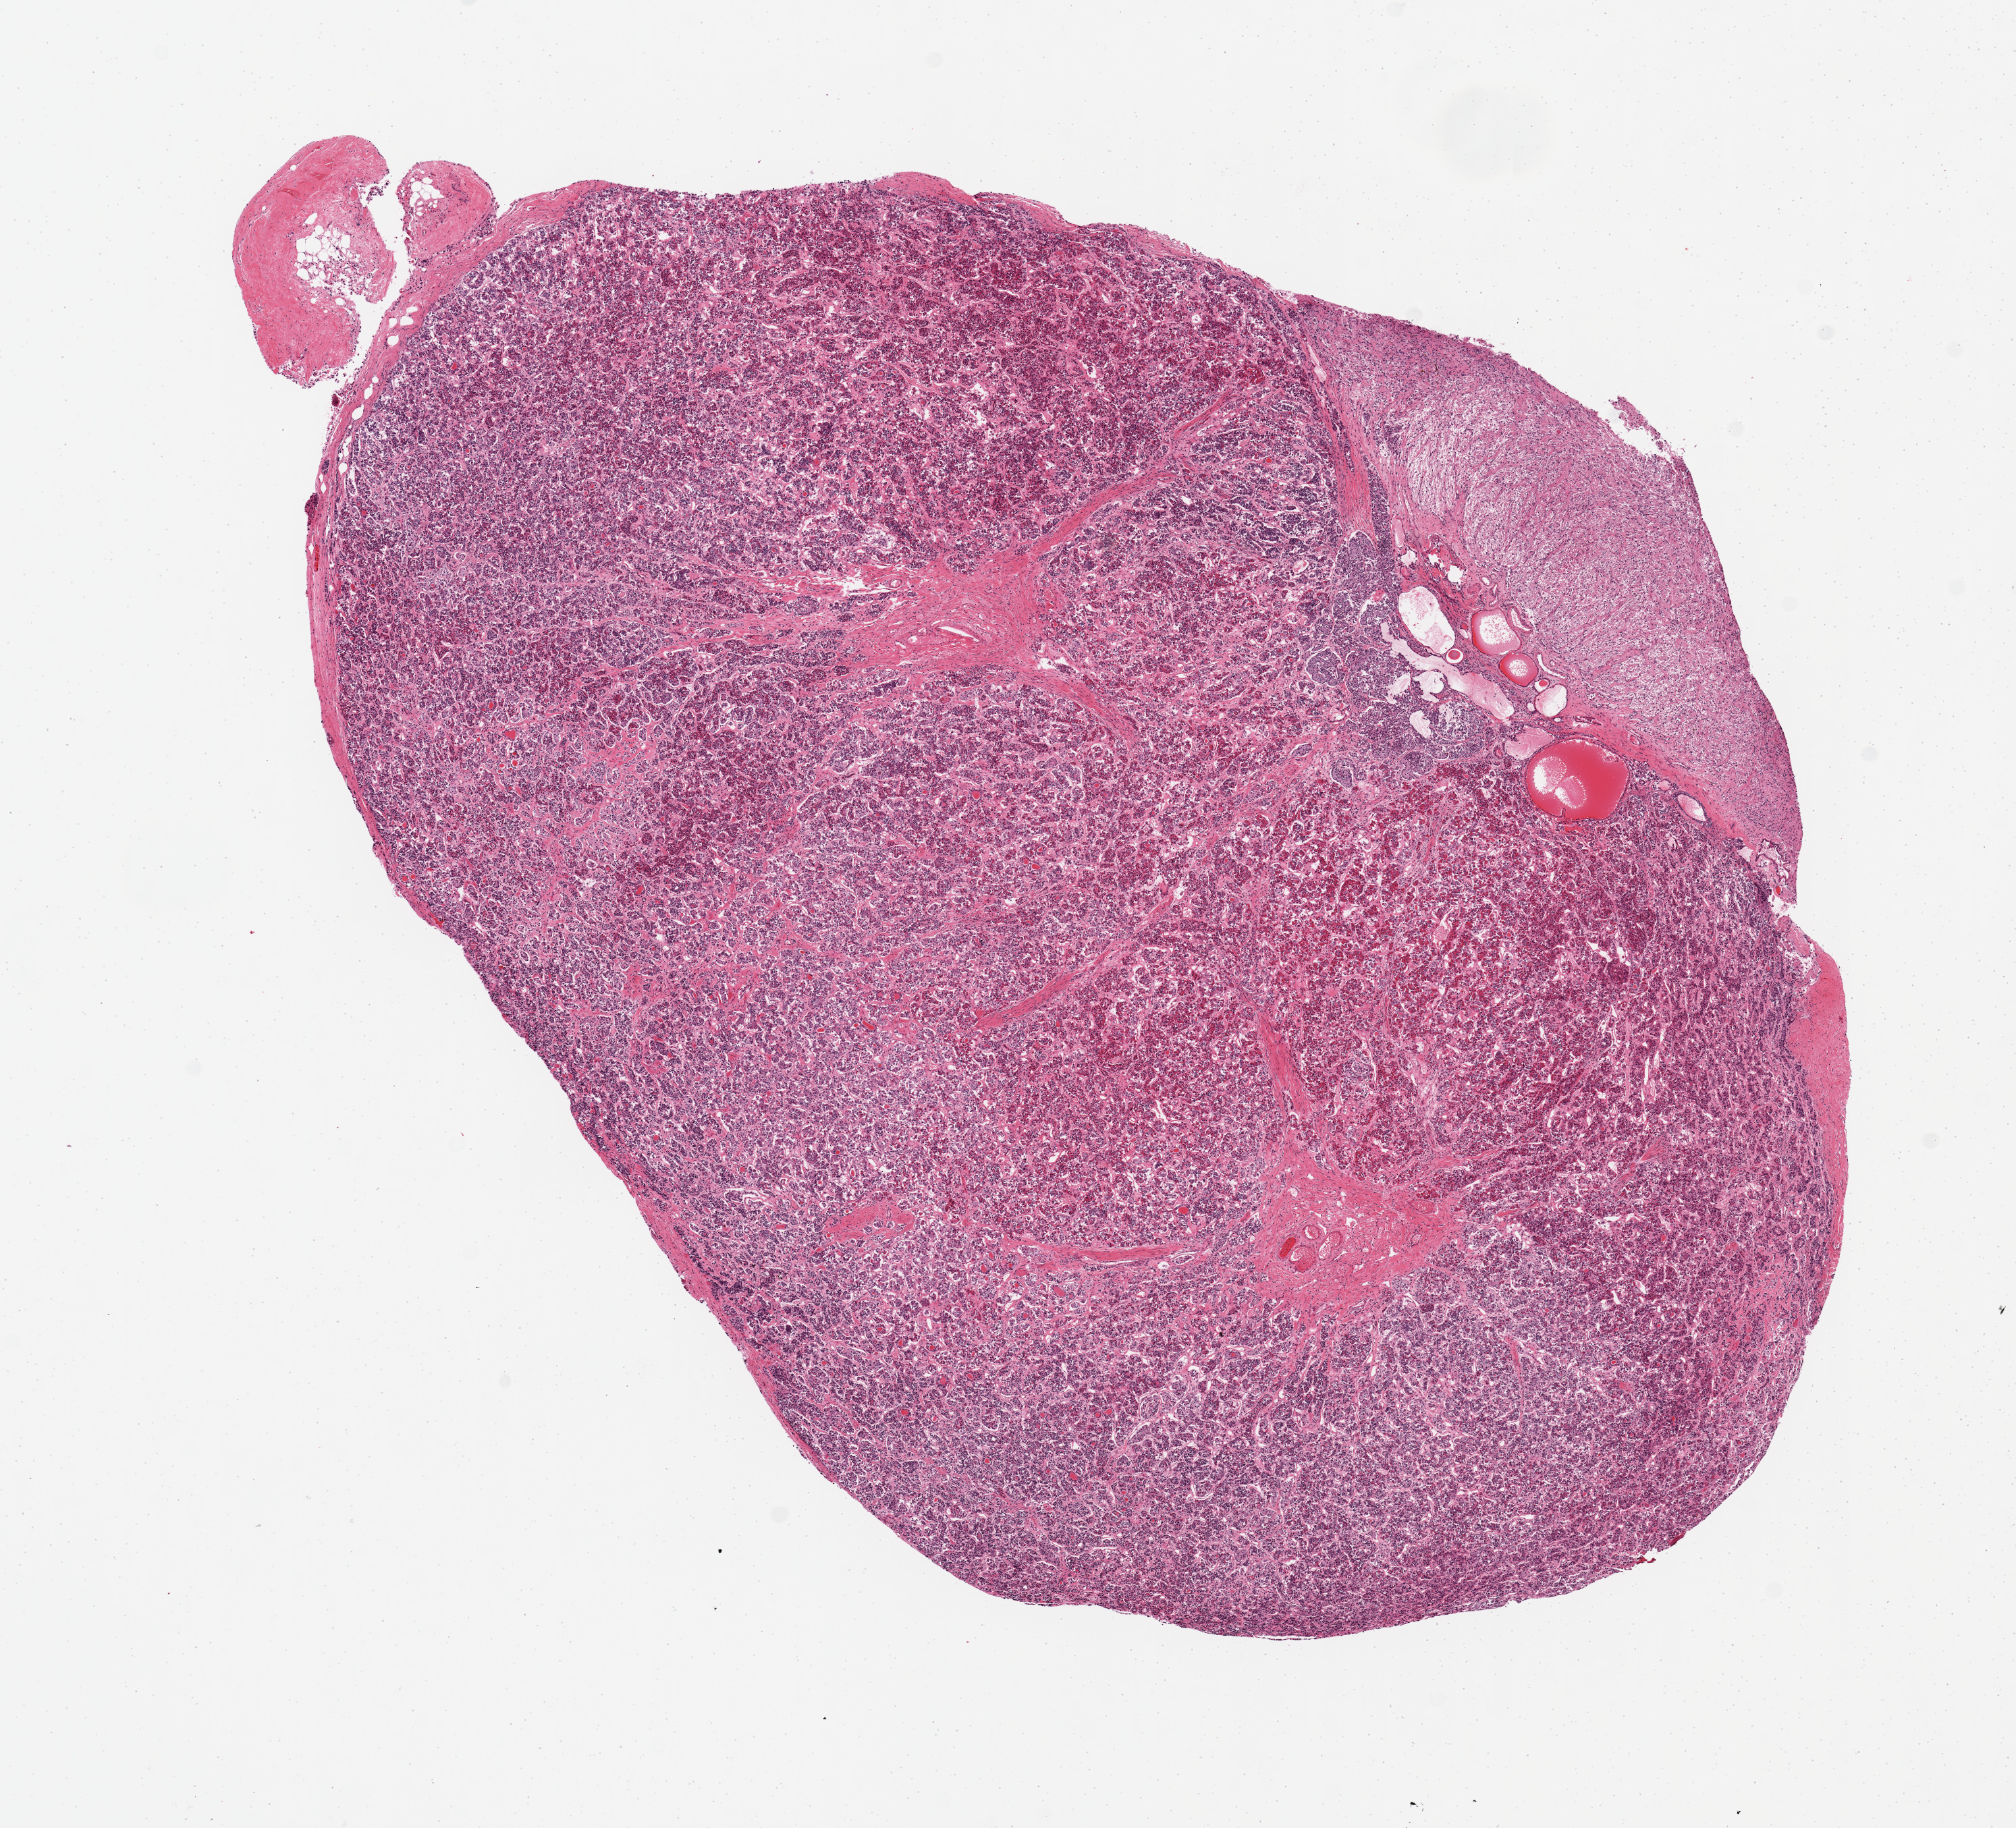
Hematoxylin and eosin (H&E) whole-slide image, brightfield — whole scanned area (about 11.8 x 10.7 mm, from a 20x scan) shown as a low-resolution overview; PAXgene-fixed, paraffin-embedded tissue; sampled site (target tissue): pituitary; donor tissue sample. Male donor.
• reviewer comment on this tissue sample: 1 piece; mostly anterior; posterior